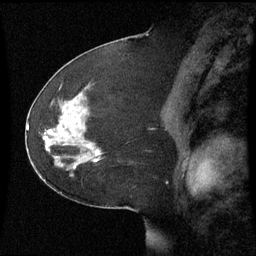
Breast MRI (dynamic contrast-enhanced), one sagittal slice. Position 33 of 60 along the scan axis. Dynamic contrast-enhanced series, image 2 of 3 at this slice position (ordered by acquisition). 1.5 T. TE 4.2 ms, TR 8.9 ms. 256 × 256 image matrix, field of view 220 × 220 mm. Female patient, age 51 years. From the clinical record (not read from this slice): setting: breast cancer imaged before/during neoadjuvant chemotherapy; receptor status: HR-positive, HER2-negative.
Structures marked on this image (semi-automatic segmentation, software-assisted and operator-edited):
- analysis volume of interest (the breast-tissue region the enhancement analysis was run in; not a lesion): box from (x=44, y=102) to (x=105, y=169) px
- tumour enhancement mask (voxels above the 70 % enhancement threshold inside the analysis volume of interest): (x=88, y=146)–(x=97, y=161)